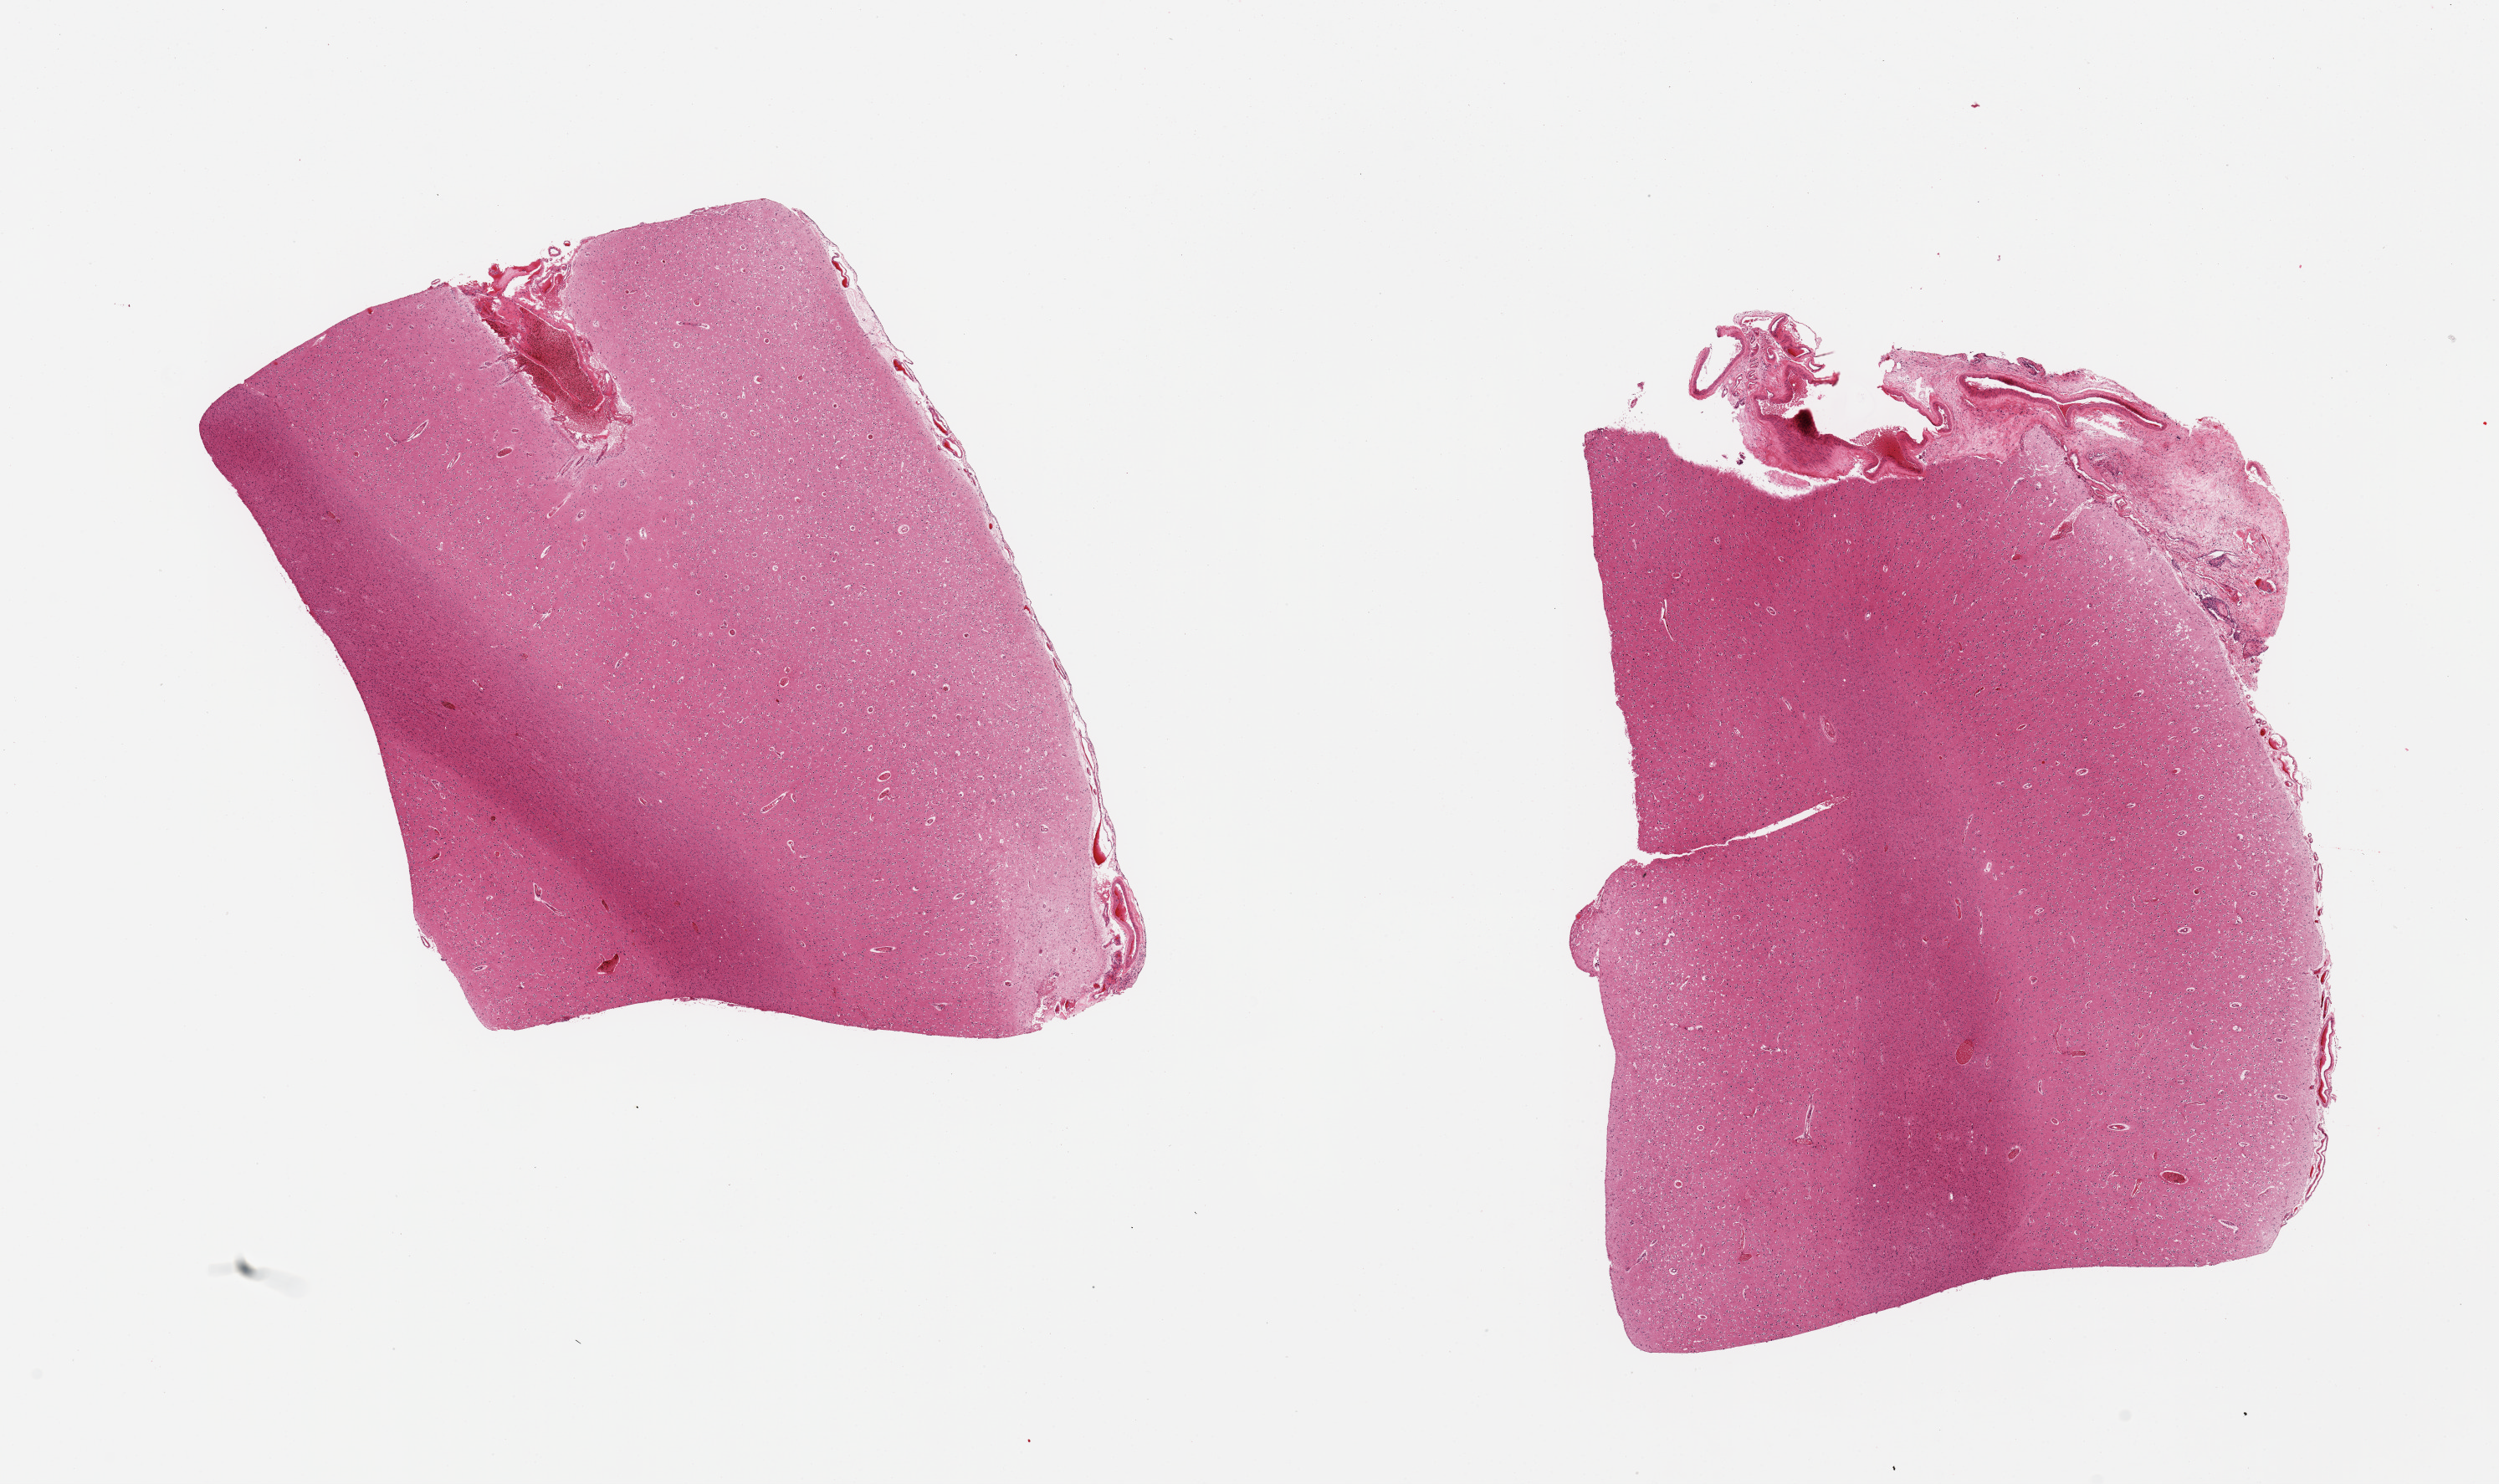
Whole-slide image, haematoxylin and eosin stain, brightfield — a low-resolution overview of the entire scanned area, about 23.6 x 14.0 mm (acquisition: 20x scan), PAXgene-fixed paraffin-embedded (PFPE) section, section of cerebral cortex (target tissue), tissue donor sample. Donor: female.
• reviewer comment on this tissue sample: 2 pieces; adherent meninges